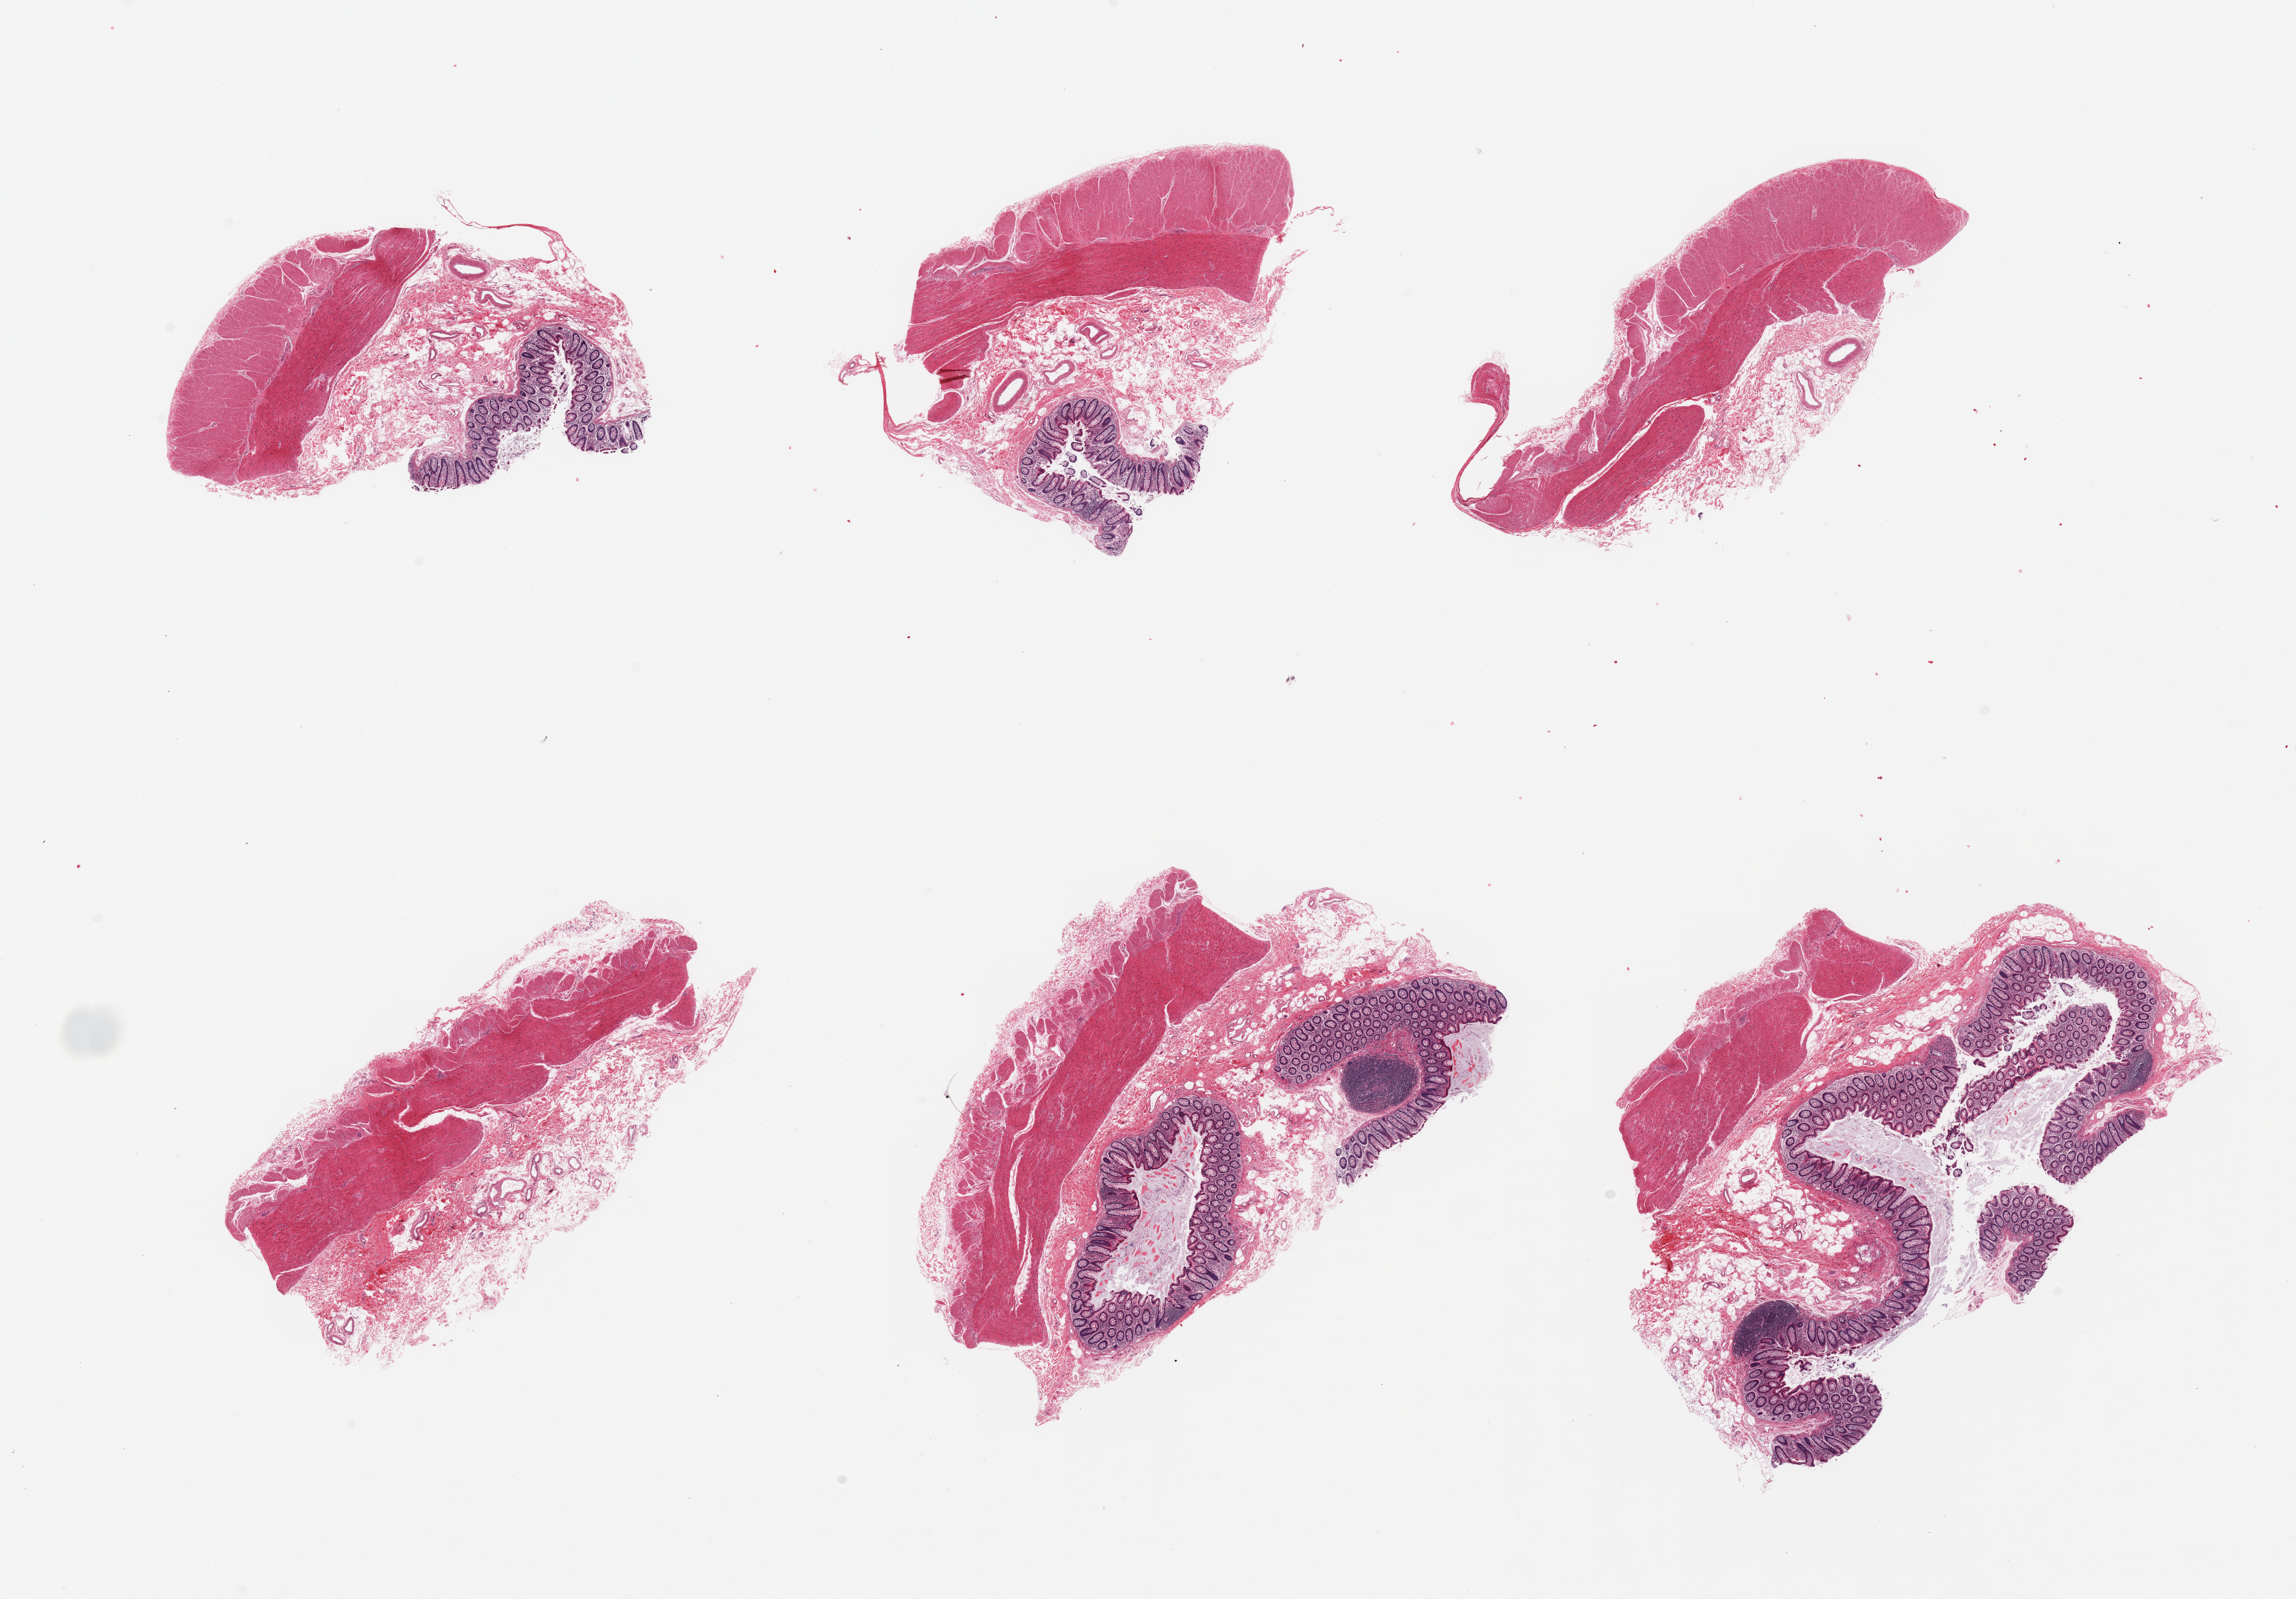
Whole-slide image, haematoxylin and eosin stain, a low-resolution overview of the entire scanned area, about 25.6 x 17.8 mm; PAXgene-fixed, paraffin-embedded tissue; sampled site (target tissue): transverse colon; donor tissue sample. Male donor.
Reviewer comment on this tissue sample: 6 pieces; 4 pieces have full thickness elements with well preserved mucosa; 2 have no mucosa (in this section).